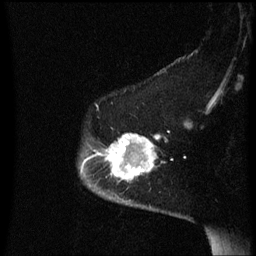
Breast MRI (dynamic contrast-enhanced), one sagittal slice. Position 49 of 60 along the scan axis. Dynamic contrast-enhanced series, image 2 of 3 at this slice position (ordered by acquisition). 1.5 T. TE 4.2 ms, TR 8.4 ms. 256 × 256 image matrix, field of view 200 × 200 mm. Female patient, age 54 years. Case-level facts recorded for this patient, not image findings: setting: breast cancer imaged before/during neoadjuvant chemotherapy; receptor status: HR-positive, HER2-negative.
Structures marked on this image (semi-automatically segmented with operator editing):
- analysis volume of interest (the breast-tissue region the enhancement analysis was run in; not a lesion): box from (x=95, y=134) to (x=161, y=191) px
- tumour enhancement mask (voxels above the 70 % enhancement threshold inside the analysis volume of interest): (x=106, y=134)–(x=160, y=181)